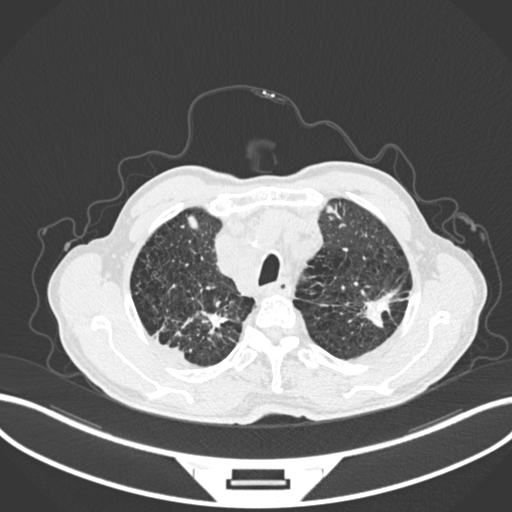
Chest CT, one axial slice. Slice 229 of 287 in the series (ordered by position). Reconstruction kernel B30f. 120 kVp. Lung window (W 1500 / L -600 HU). 1 mm slice thickness. 512 × 512 image matrix. Patient: male, 74 years. Case-level facts recorded for this patient, not image findings: clinical TNM (as recorded): T2a N1 M0.
Structures marked on this image (rectangle marked by the reading radiologist):
- lung tumour (recorded histology: adenocarcinoma): box from (x=358, y=291) to (x=408, y=329) px